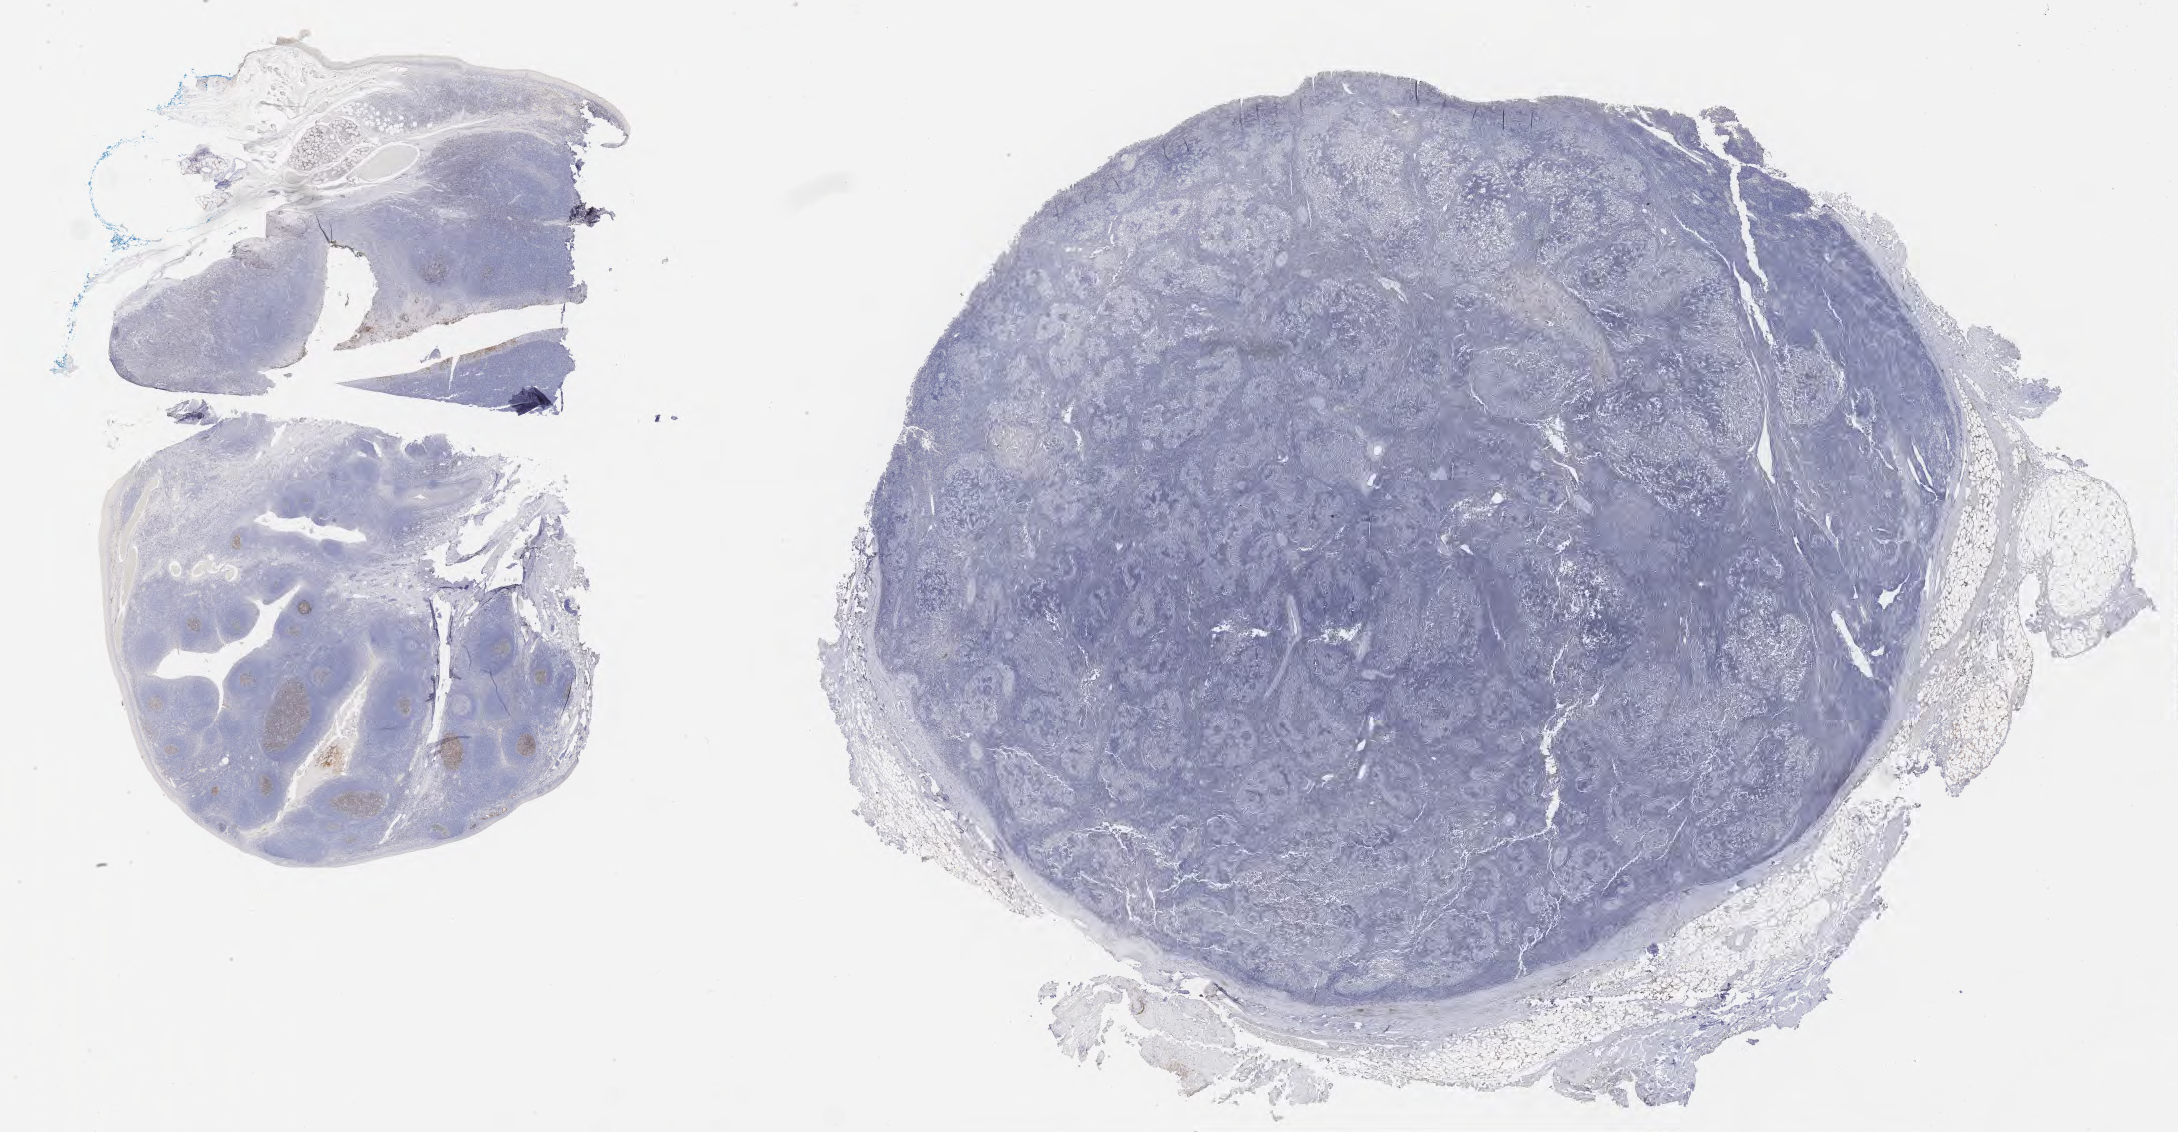
Whole-slide image, immunohistochemical stain for CD10, low-resolution overview of the scanned area, about 35.2 x 18.3 mm; tumor tissue; site: lymph node. Patient: male, aged 46.
Diagnosis: Diffuse large B-cell lymphoma, NOS.